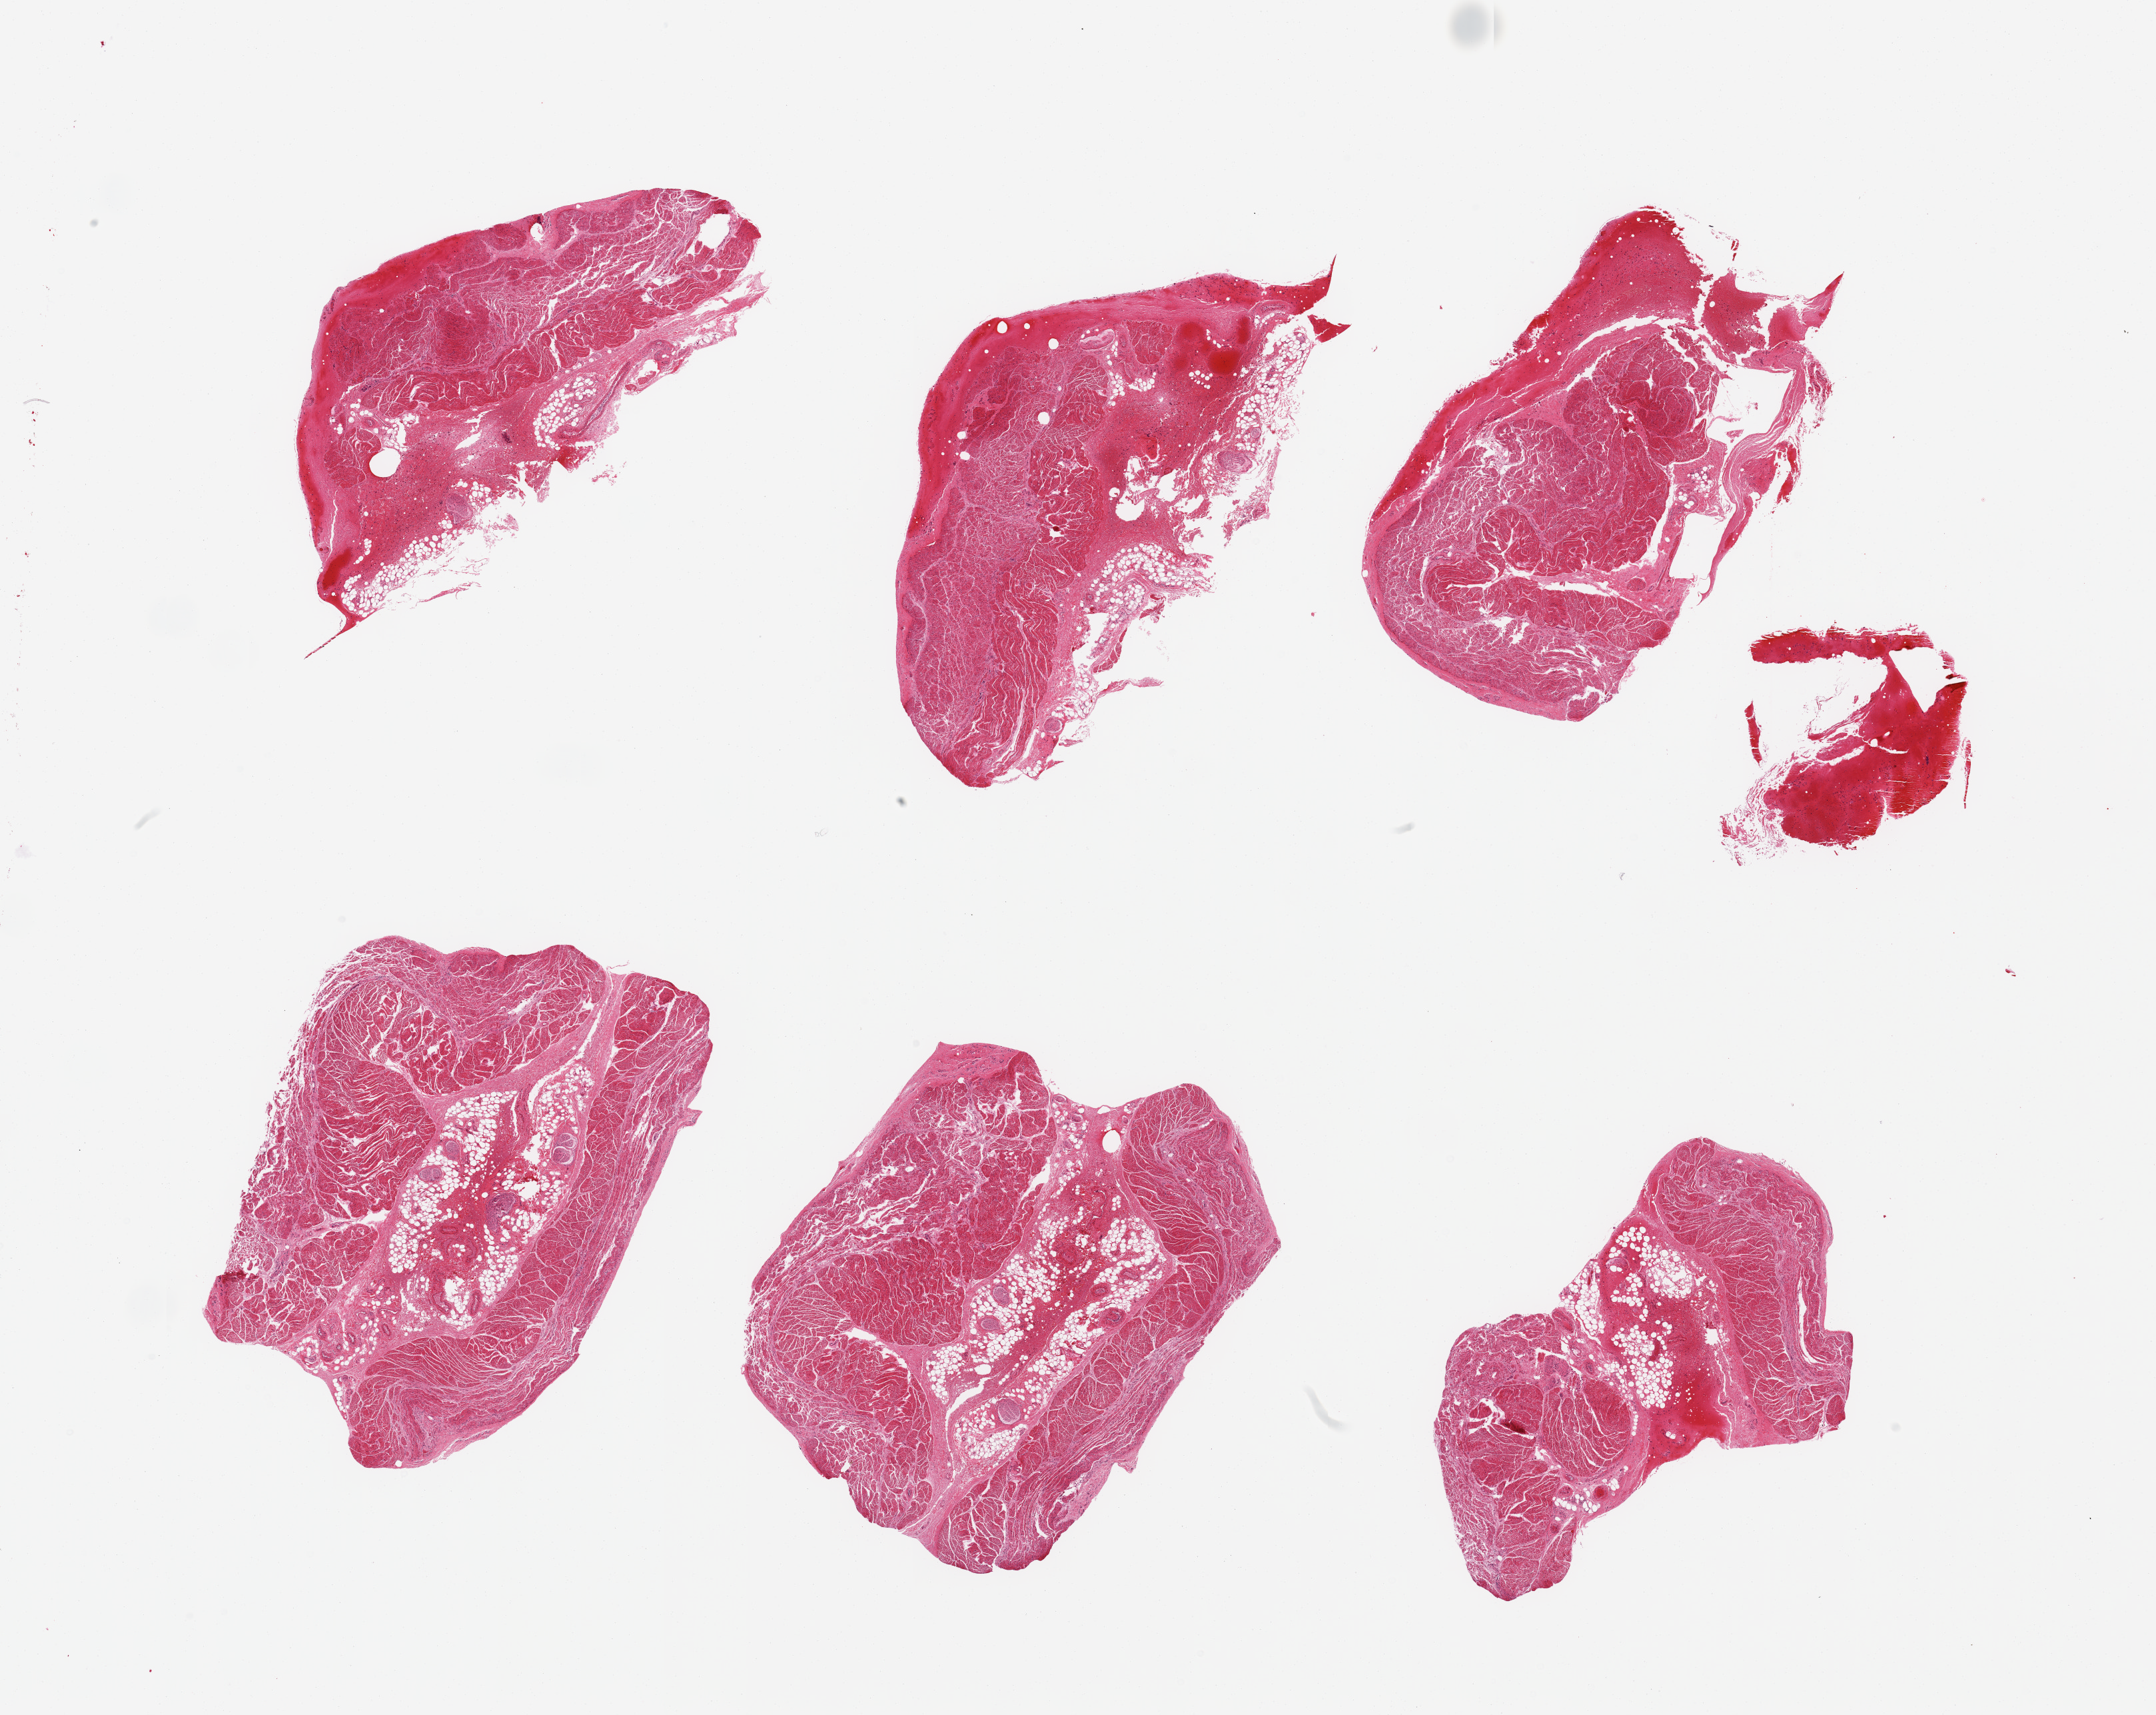
Digitized H&E-stained section — low-resolution overview of the scanned area, about 25.6 x 20.4 mm (slide scanned at 20x). PAXgene-fixed, paraffin-embedded tissue. Section of esophageal muscle (target tissue). Donor tissue sample. Donor sex: male.
Pathologist's review note for this sample: 6 pieces, confirmed target muscularis, ~25% fat.